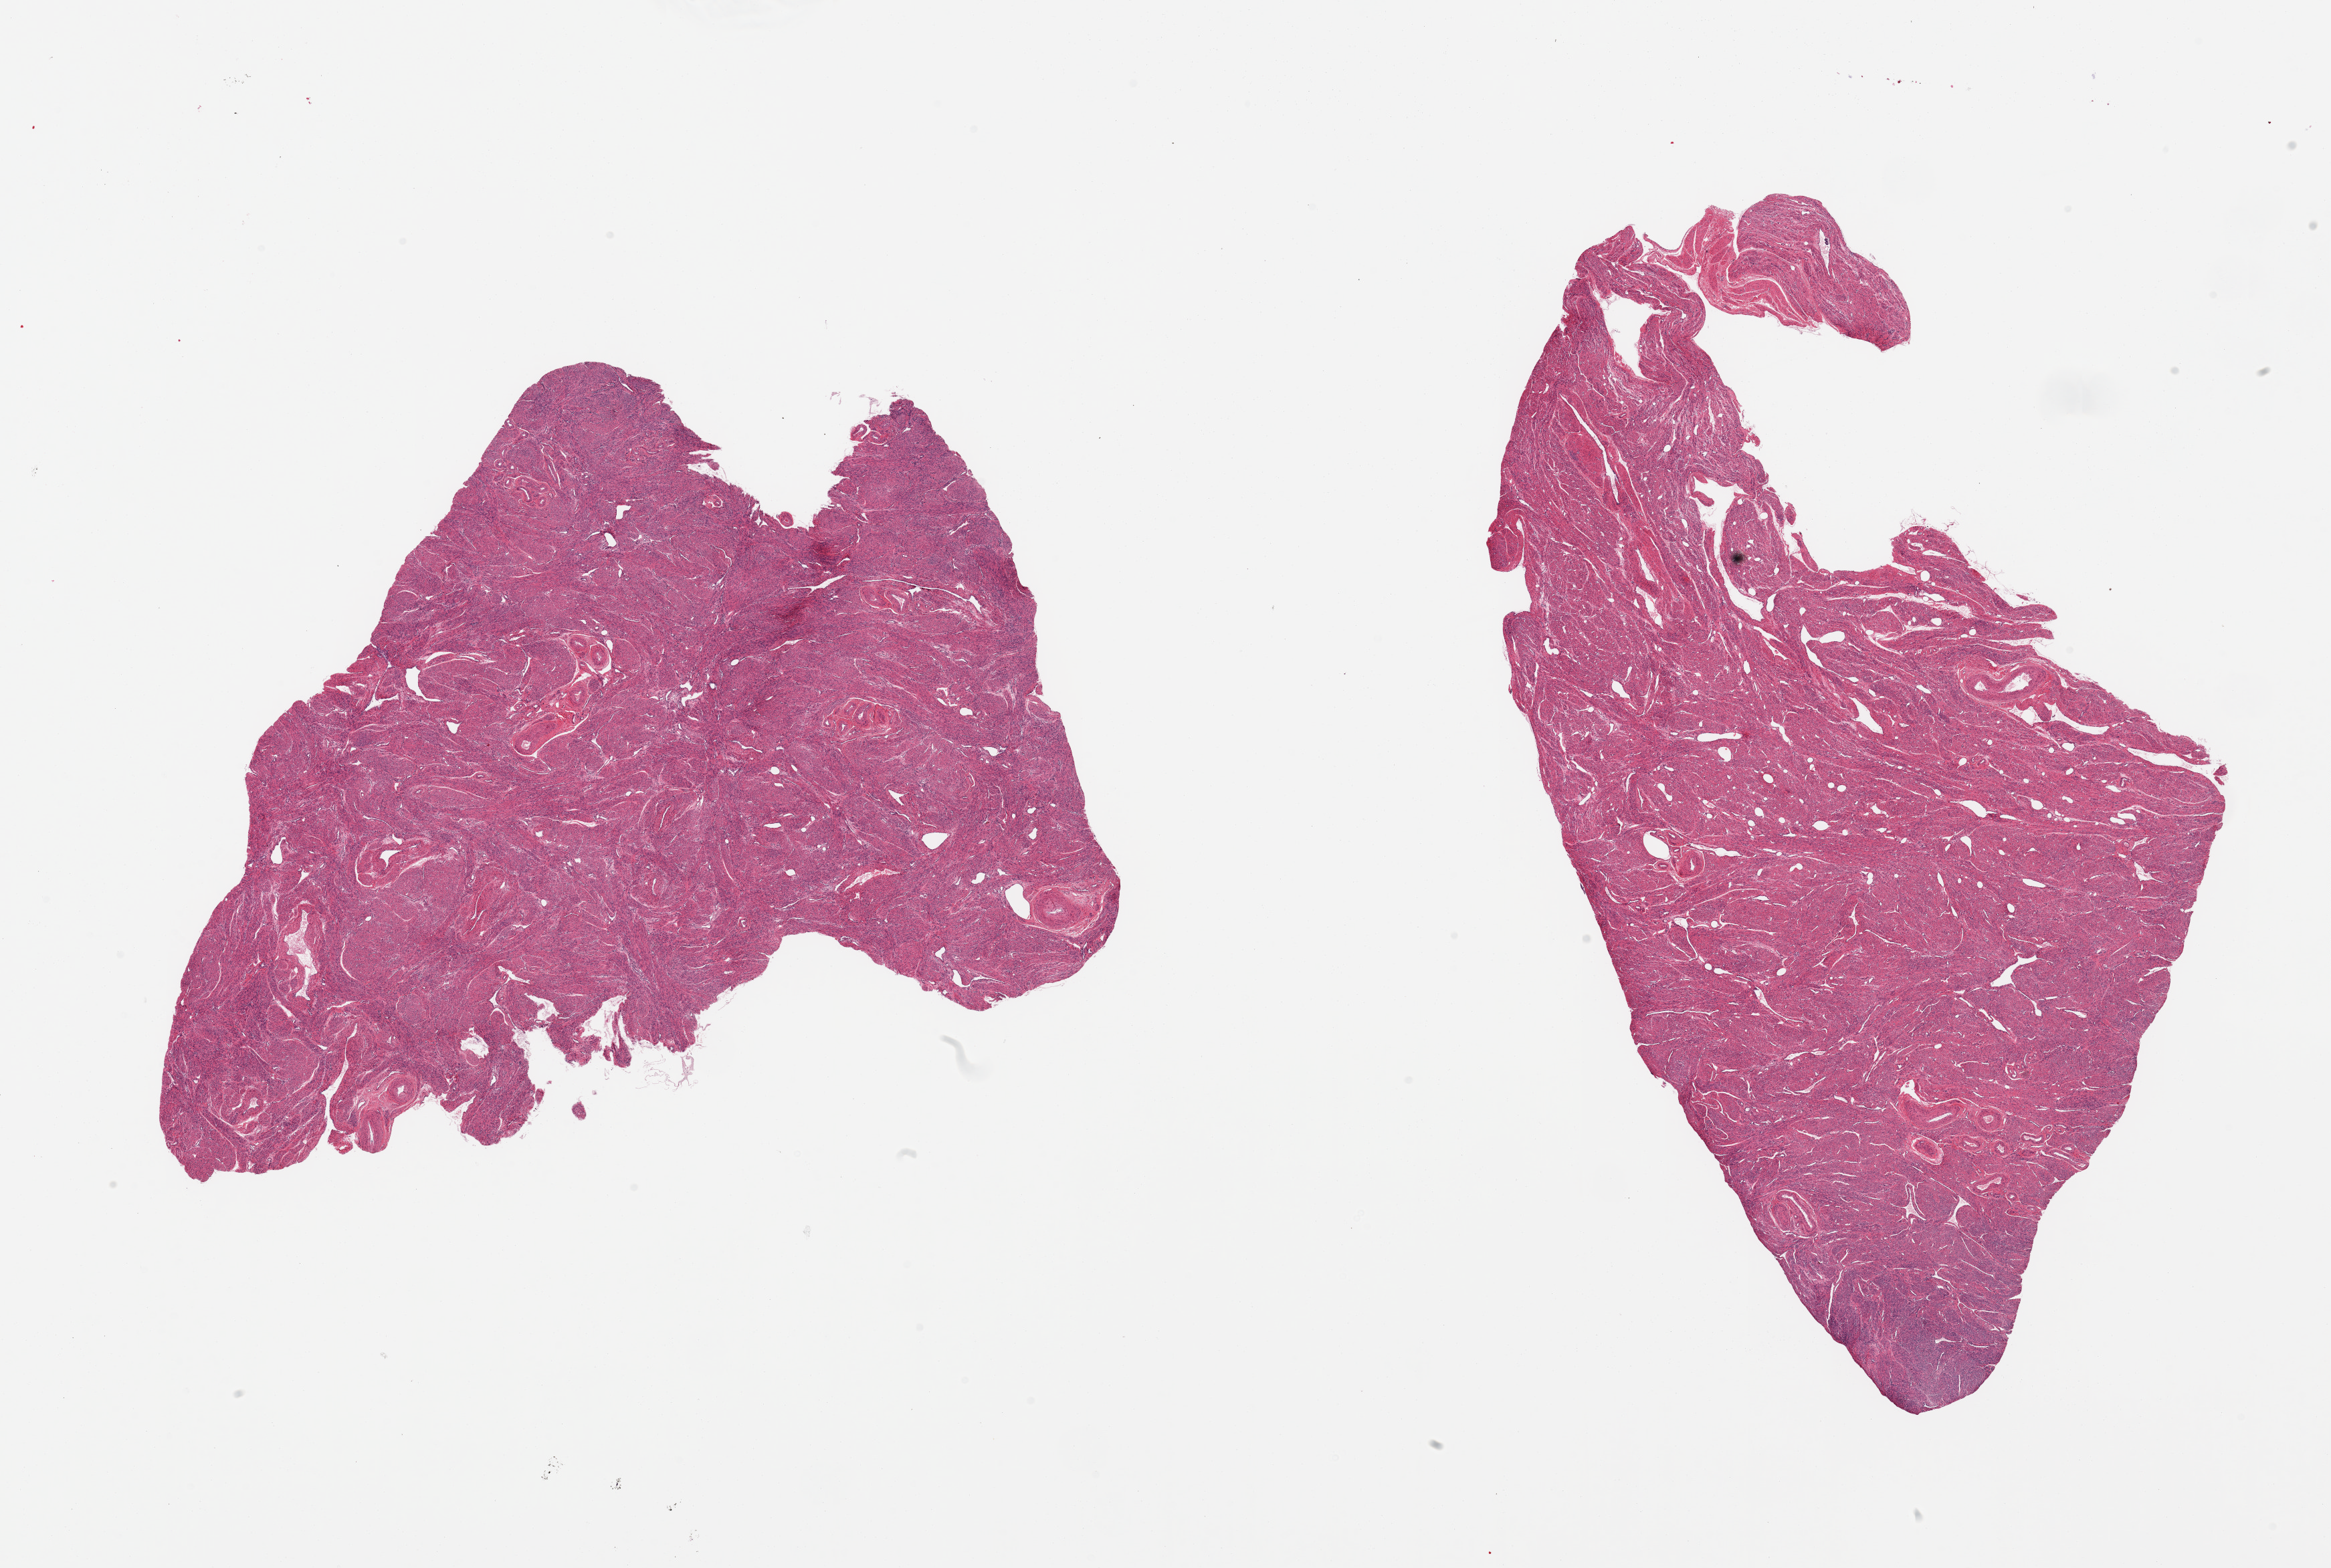
Haematoxylin and eosin whole-slide image, shown as a low-resolution overview of the whole scanned area (about 27.6 x 18.5 mm, slide scanned at 20x), PAXgene-fixed, paraffin-embedded tissue, sampled site (target tissue): uterus, tissue donor sample. Donor: female.
Pathologist's review note for this sample: 2 pieces; myometrium only in this section.